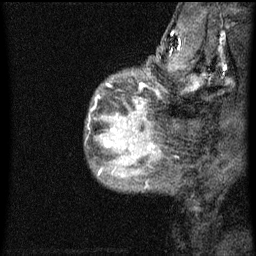
Breast MRI (dynamic contrast-enhanced), one sagittal slice; slice 11 of 60 in the series (ordered by position); dynamic contrast-enhanced series, image 2 of 3 at this slice position (ordered by acquisition); 1.5 T; TE 4.2 ms, TR 8 ms; 2 mm slice thickness; 256 × 256 image matrix, field of view 180 × 180 mm. Patient: female, 50 years.
Structures marked on this image (semi-automatically segmented with operator editing):
- analysis volume of interest (the breast-tissue region the enhancement analysis was run in; not a lesion): bounding box [x1, y1, x2, y2] px = [86, 76, 141, 187]
- tumour enhancement mask (voxels above the 70 % enhancement threshold inside the analysis volume of interest): [106, 106, 140, 147]